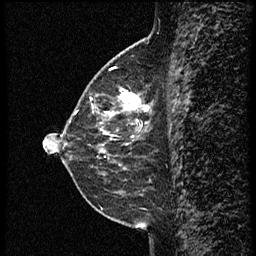
Breast MRI (dynamic contrast-enhanced), one sagittal slice. Slice 23 of 60 in the series (ordered by position). Dynamic contrast-enhanced study with each time point stored as its own series, time point 2 of 3 at this slice position (early post-contrast, ordered by acquisition time). 1.5 T. TE 4.2 ms, TR 18.9 ms. 2 mm slice thickness. 256 × 256 image matrix, field of view 200 × 200 mm. Female patient. From the clinical record (not read from this slice): setting: breast cancer imaged before/during neoadjuvant chemotherapy; receptor status: HER2-positive.
Structures marked on this image (semi-automatic segmentation, software-assisted and operator-edited):
- analysis volume of interest (the breast-tissue region the enhancement analysis was run in; not a lesion): bounding box <77,86,160,147> (left, top, right, bottom; pixels)
- tumour enhancement mask (voxels above the 100 % enhancement threshold inside the analysis volume of interest): <89,89,152,147>